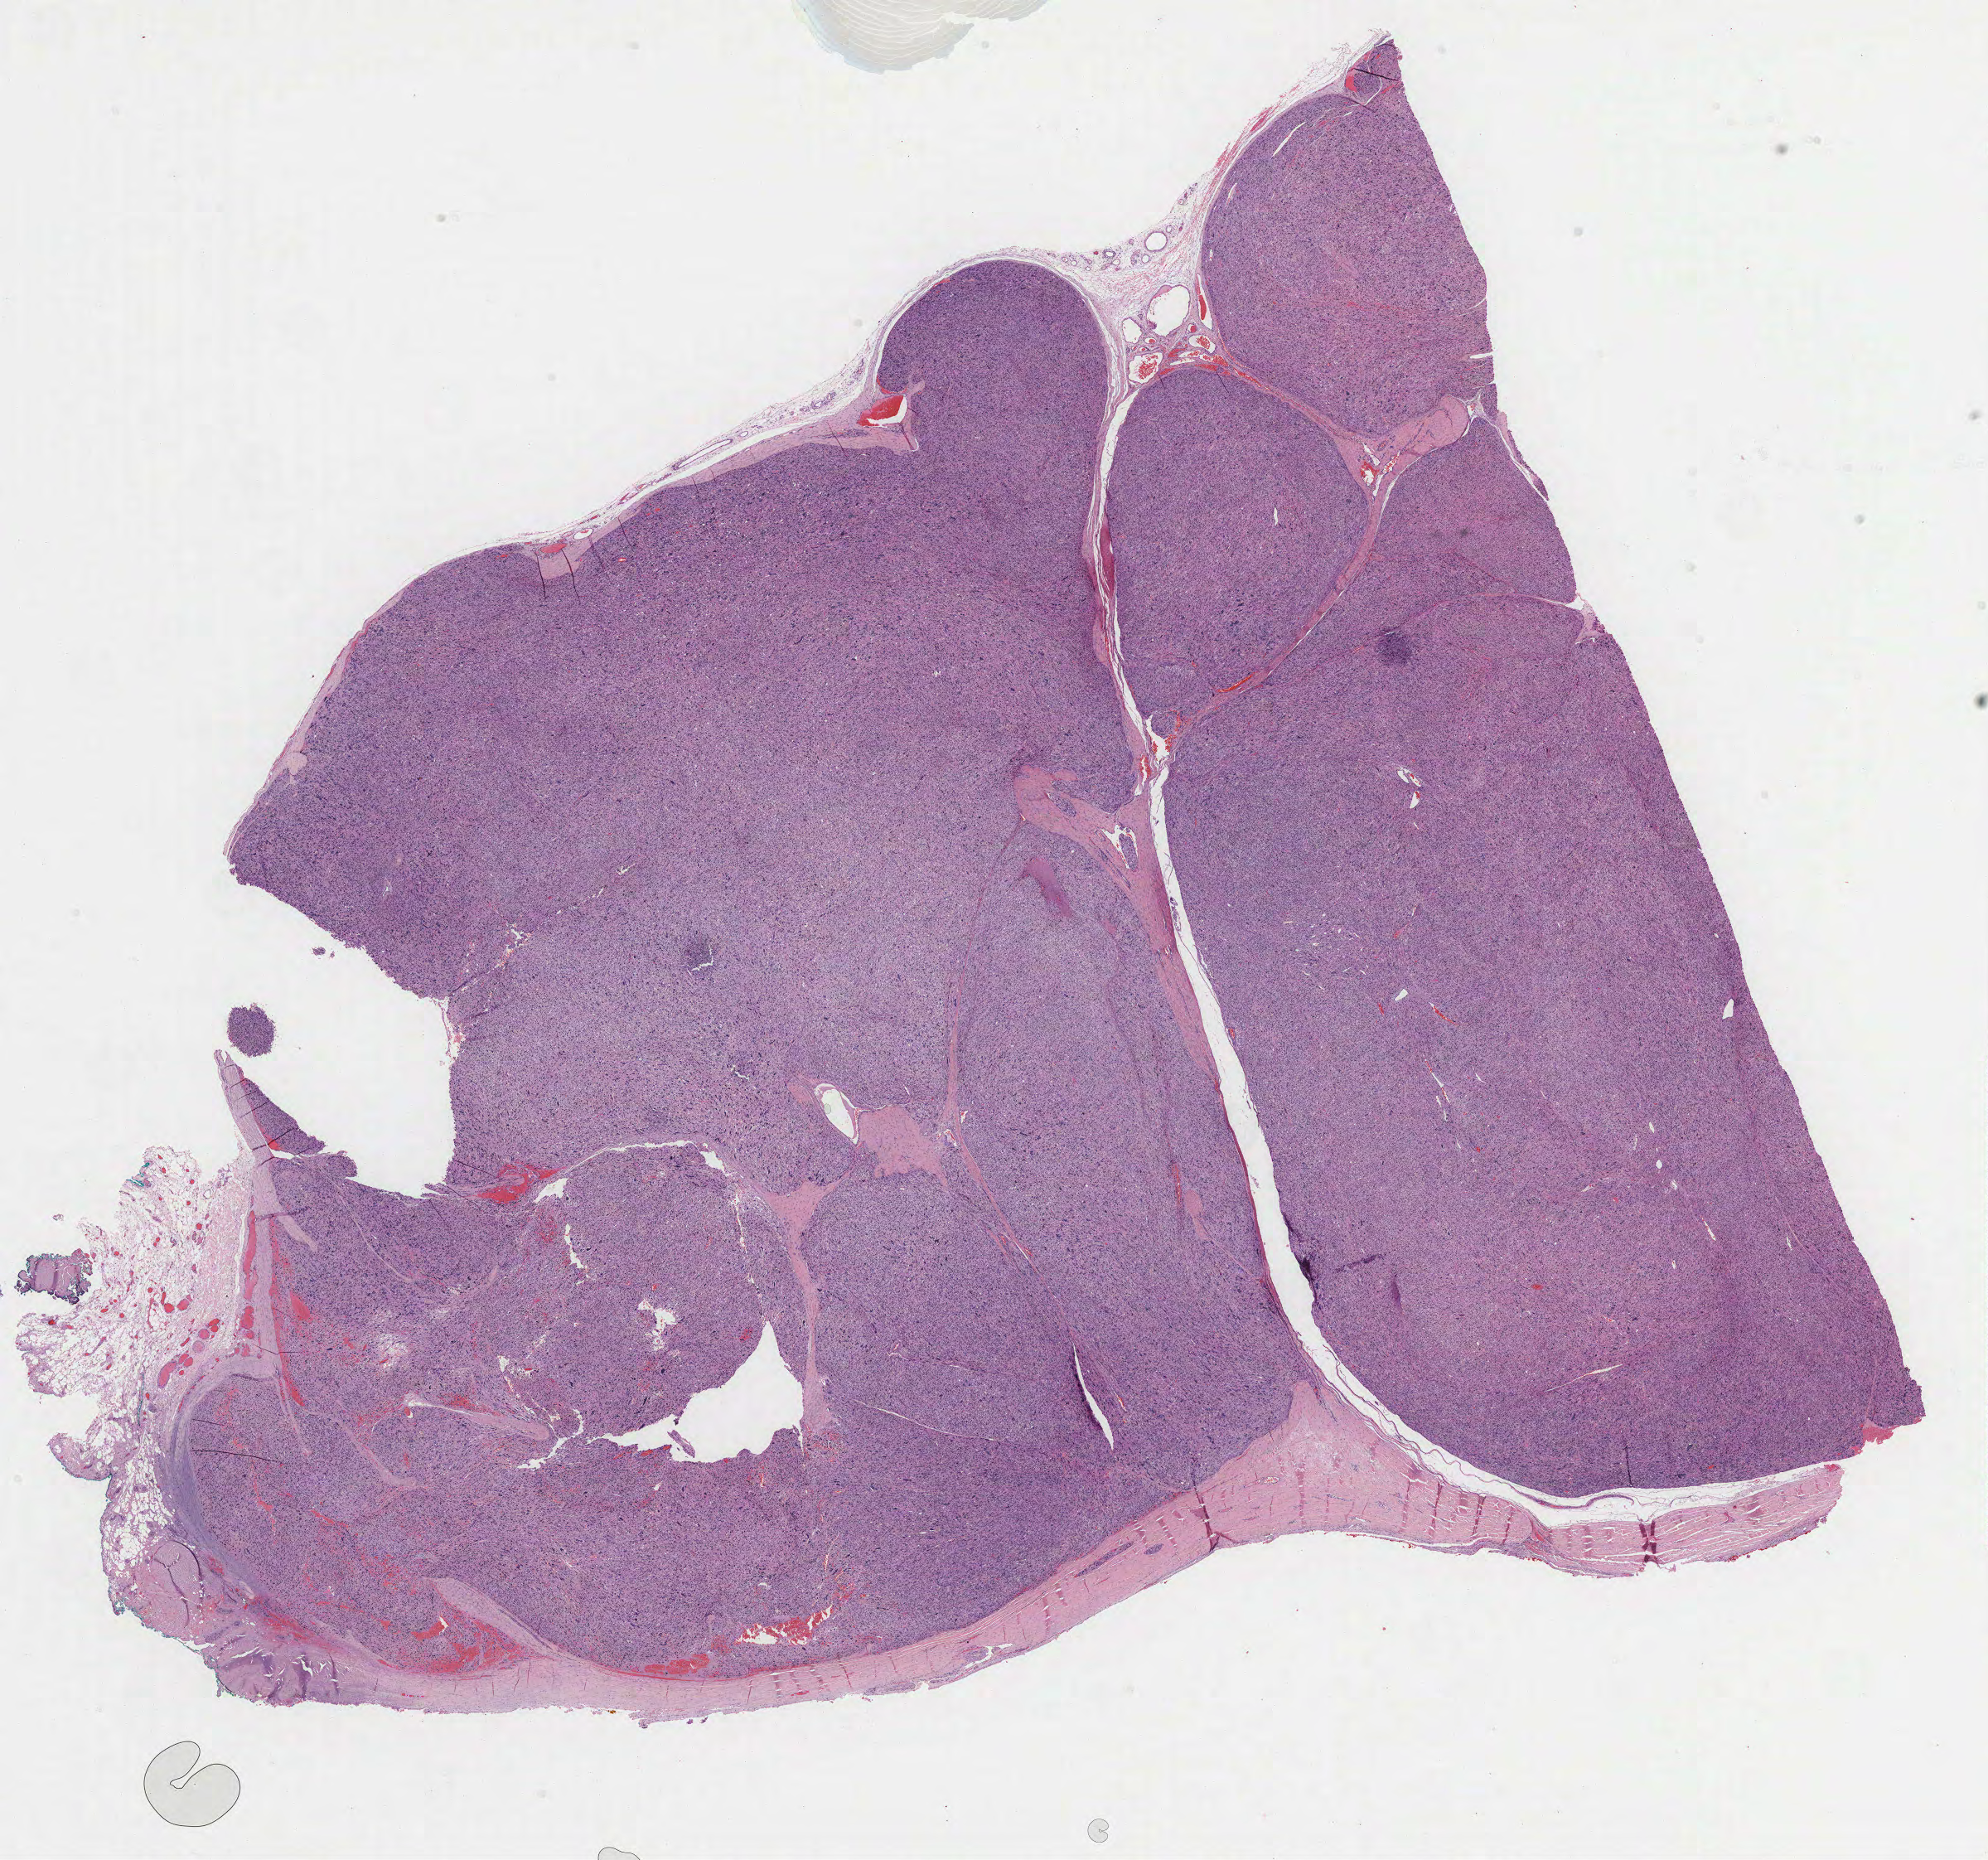
Digitized H&E-stained tissue section (whole slide) — whole scanned area (about 19.4 x 18.1 mm, acquisition: 40x scan) shown as a low-resolution overview, FFPE section, connective, subcutaneous and other soft tissues, primary tumour sample. Female patient; age at initial diagnosis 38 years.
Diagnosis: Leiomyosarcoma, NOS (connective, subcutaneous and other soft tissues of lower limb and hip).